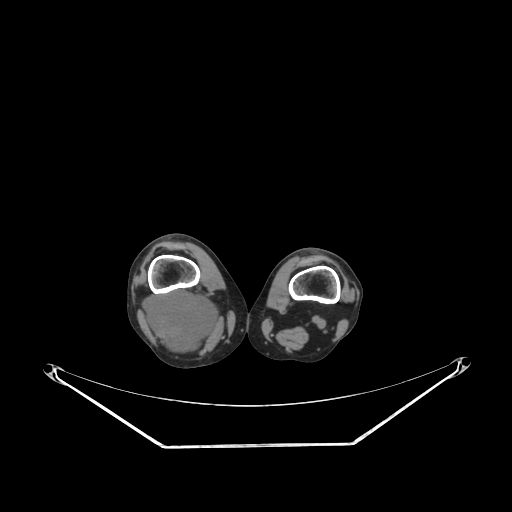
CT of an extremity soft-tissue mass (from a PET/CT study), one axial slice. Position 179 of 267 along the scan axis. Reconstruction kernel SOFT. 140 kVp. Soft-tissue window (W 400 / L 40 HU). 512 × 512 image matrix, field of view 500 × 500 mm. Female patient. Case-level facts recorded for this patient, not image findings: histological type: liposarcoma; site of the primary tumour: right thigh.
Structures marked on this image (expert contour drawn on MRI and transferred to this co-registered scan by the dataset authors):
- gross tumour volume (mass): bounding box <142,290,220,355> (left, top, right, bottom; pixels)